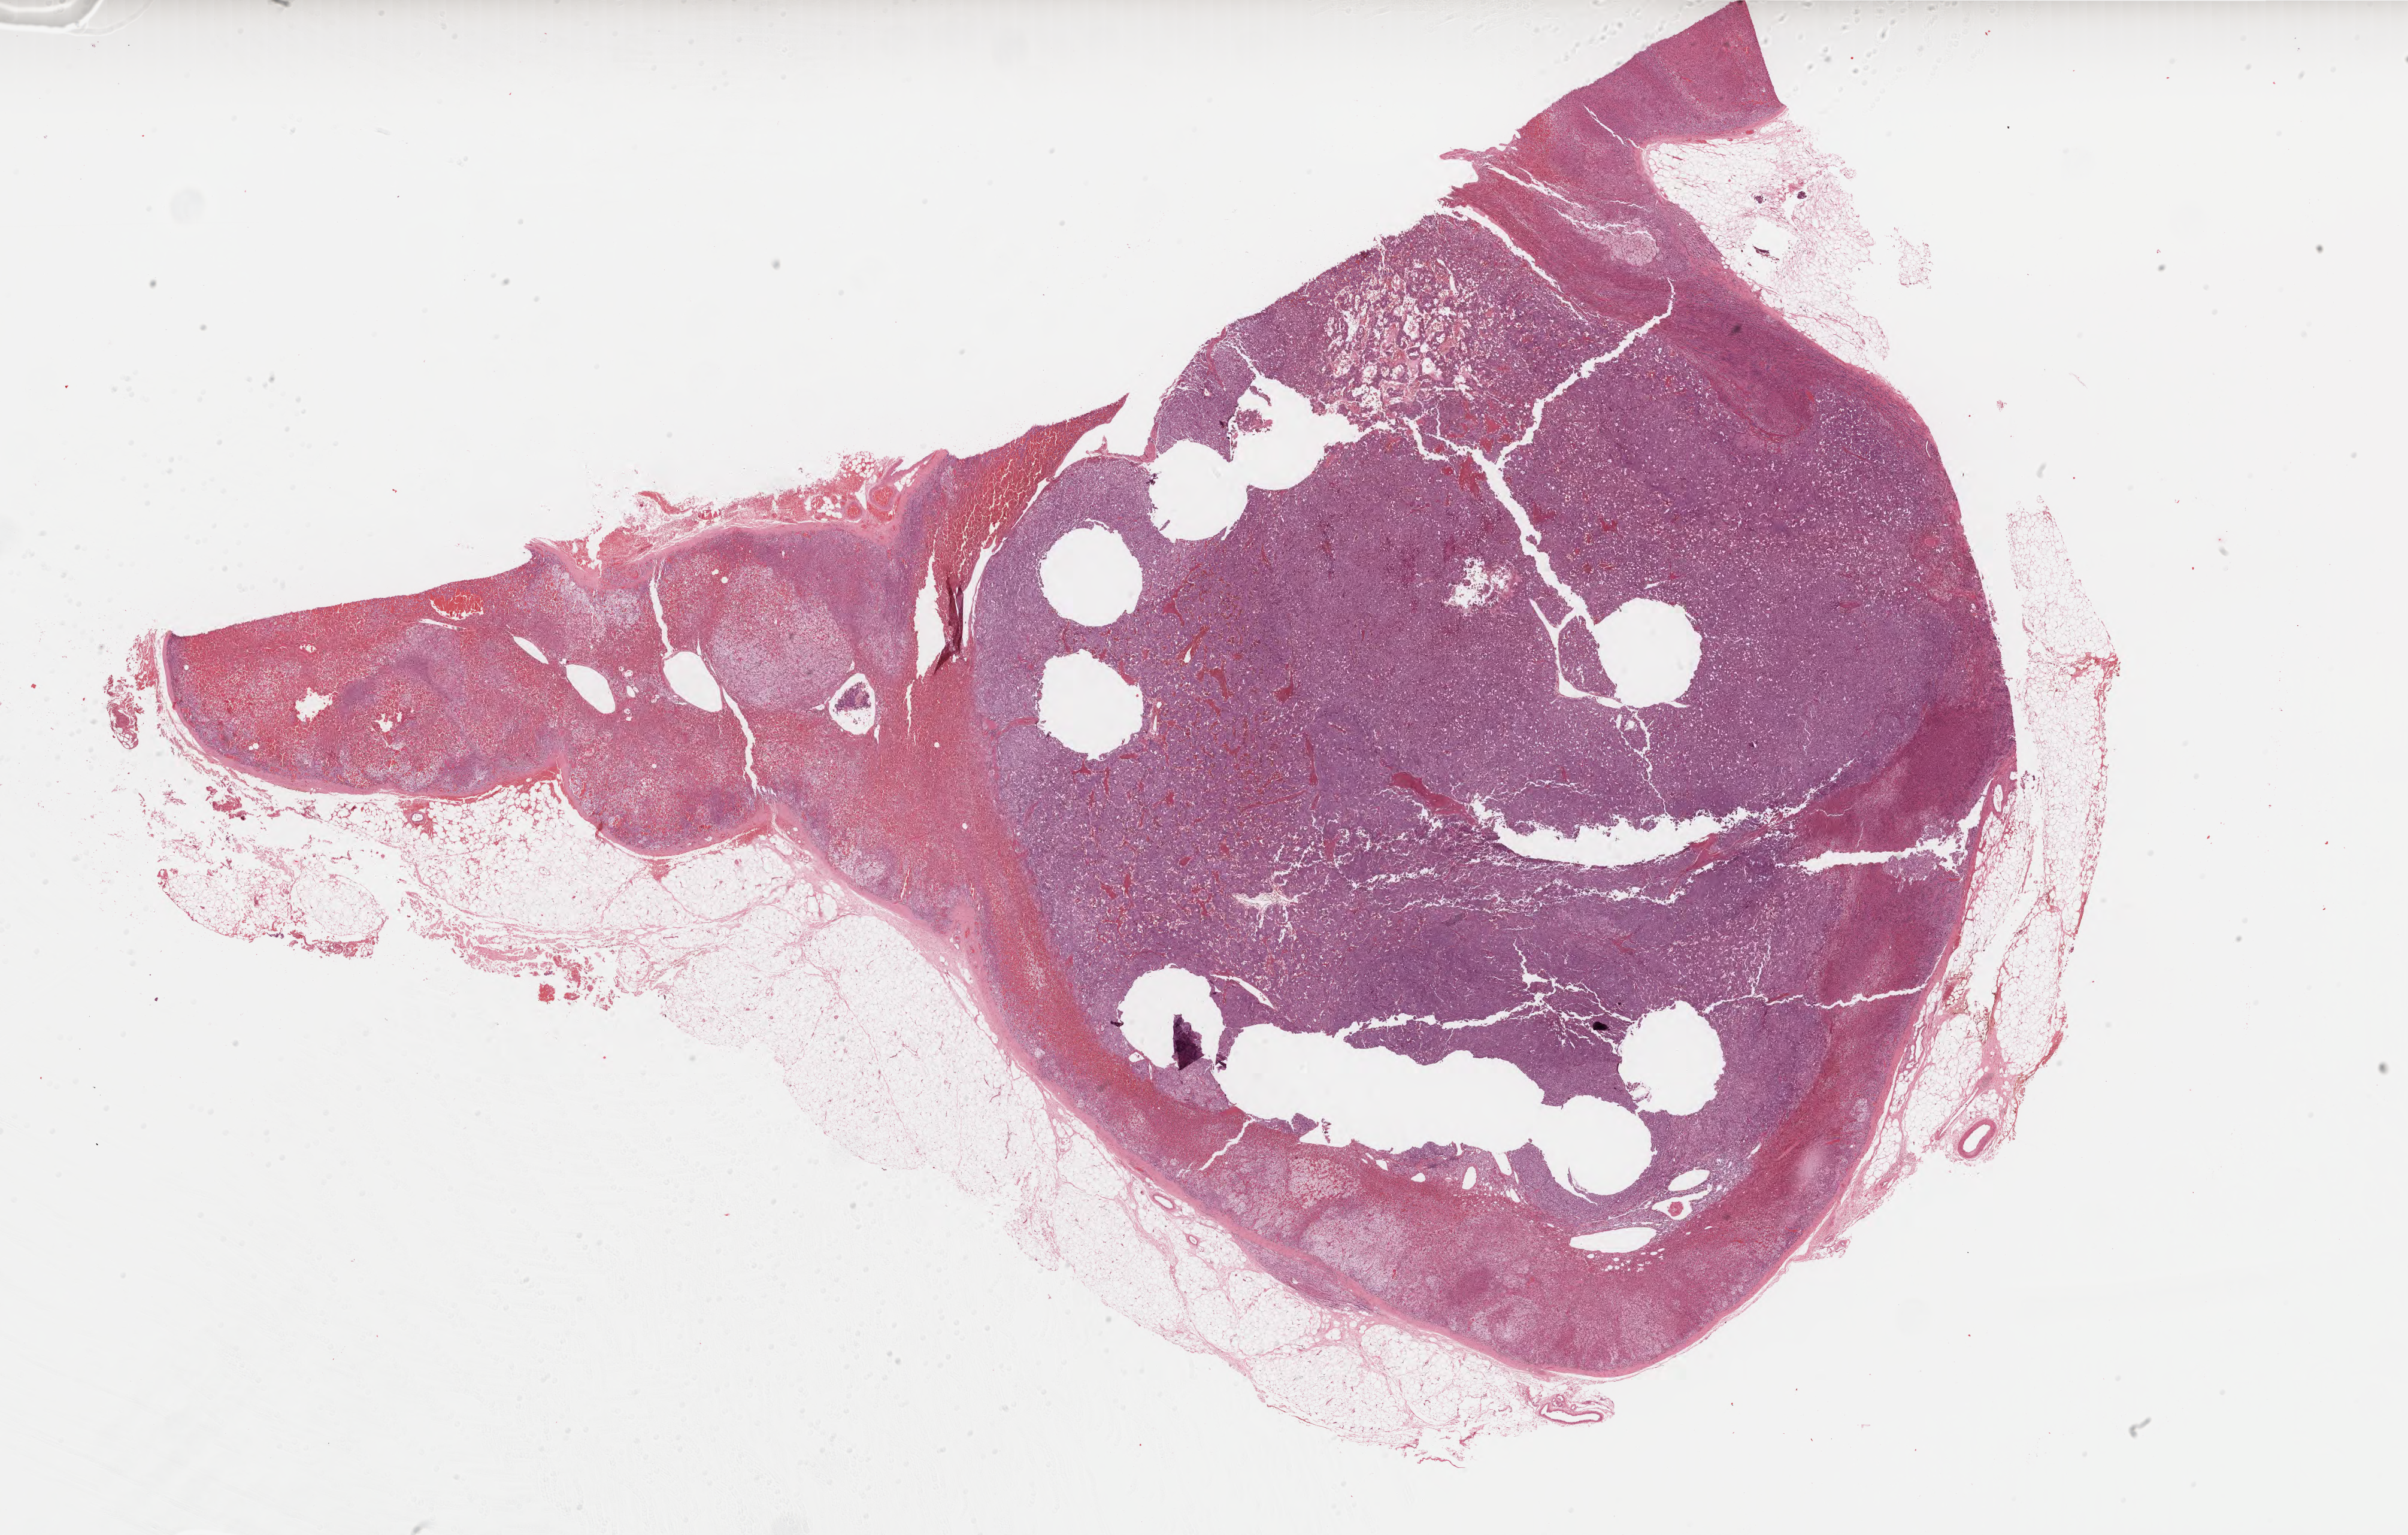
H&E-stained whole-slide image, whole scanned area (about 32.4 x 20.6 mm) shown as a low-resolution overview, formalin-fixed paraffin-embedded (FFPE) diagnostic section, sample: primary tumour, adrenal gland. Male patient; age at initial diagnosis 48 years.
Laterality: right. Diagnosis: Pheochromocytoma, NOS.